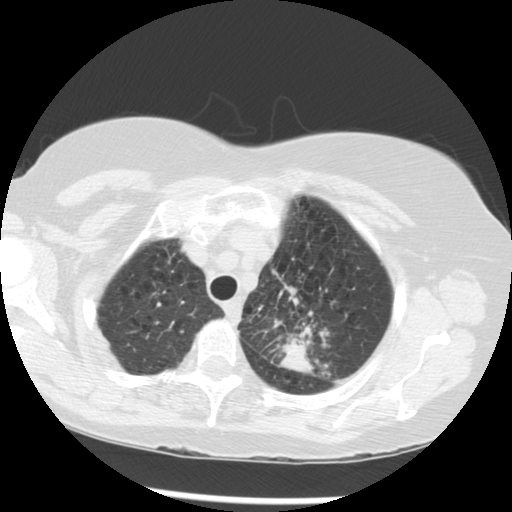
Low-dose screening chest CT, one axial slice. Slice 235 of 283 in the series (ordered by position). 120 kVp. Lung window (W 1500 / L -600 HU). 512 × 512 image matrix.
Structures marked on this image (manually delineated by an expert):
- lesion 1 (tumor, upper lobe of left lung): bounding box <279,329,315,376> (left, top, right, bottom; pixels)